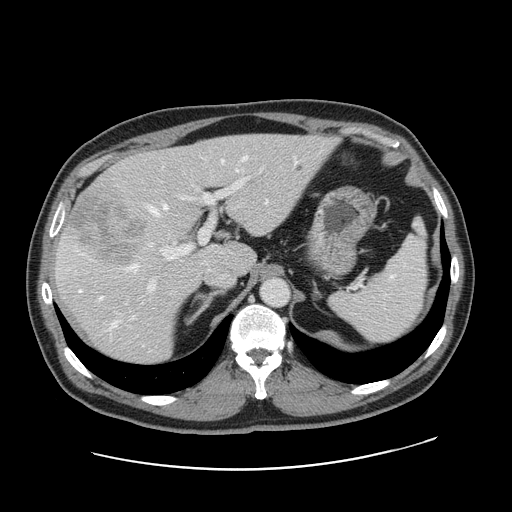
Contrast-enhanced abdominal CT, one axial slice. 120 kVp. Intravenous contrast given. Soft-tissue window (W 400 / L 40 HU). 2.5 mm slice thickness. 512 × 512 image matrix, field of view 403 × 403 mm. Male patient, age 63 years. From the clinical record (not read from this slice): diagnosis: colorectal cancer liver metastases, imaged before liver resection; multiple liver metastases: yes; largest metastasis: 8 cm; disease in both lobes: yes.
Outlined on this slice (expert manual segmentation):
- hepatic veins: bounding box [x1, y1, x2, y2] px = [79, 156, 247, 327]
- liver: [52, 135, 333, 366]
- planned liver remnant (the part of the liver to remain after resection): [135, 135, 333, 274]
- portal vein (with intrahepatic branches): [148, 170, 261, 291]
- liver metastasis: [297, 165, 303, 172]
- liver metastasis: [70, 195, 148, 271]